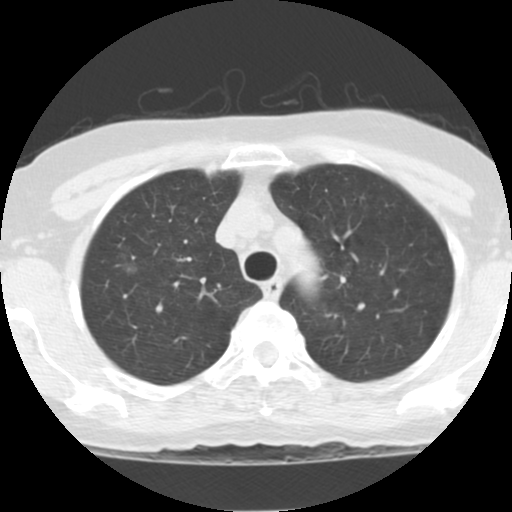
Low-dose screening chest CT, axial slice; second annual screen; lung window (W 1500 / L -600 HU); standard (soft-tissue) reconstruction kernel (STANDARD); slice 24 of 118 in the series. Female, age 62 years at enrolment.
Lesion marked by an expert reader, bounding box (x1, y1, x2, y2) in pixels: (105, 249, 151, 296). The exam's reader record, not a measurement of the box and not confirmed to be the same lesion: non-calcified nodule or mass ≥4 mm, right upper lobe, 8 × 7 mm, poorly defined margins, ground glass attenuation, pre-existing on the prior screen: yes; interval growth: yes. Official screen result: positive, other. Later outcome: lung cancer diagnosed 433 days after this screen (after the third annual screen) — bronchiolo-alveolar adenocarcinoma, NOS, right upper lobe, stage IA (AJCC 6th edition), 10 mm at pathology.